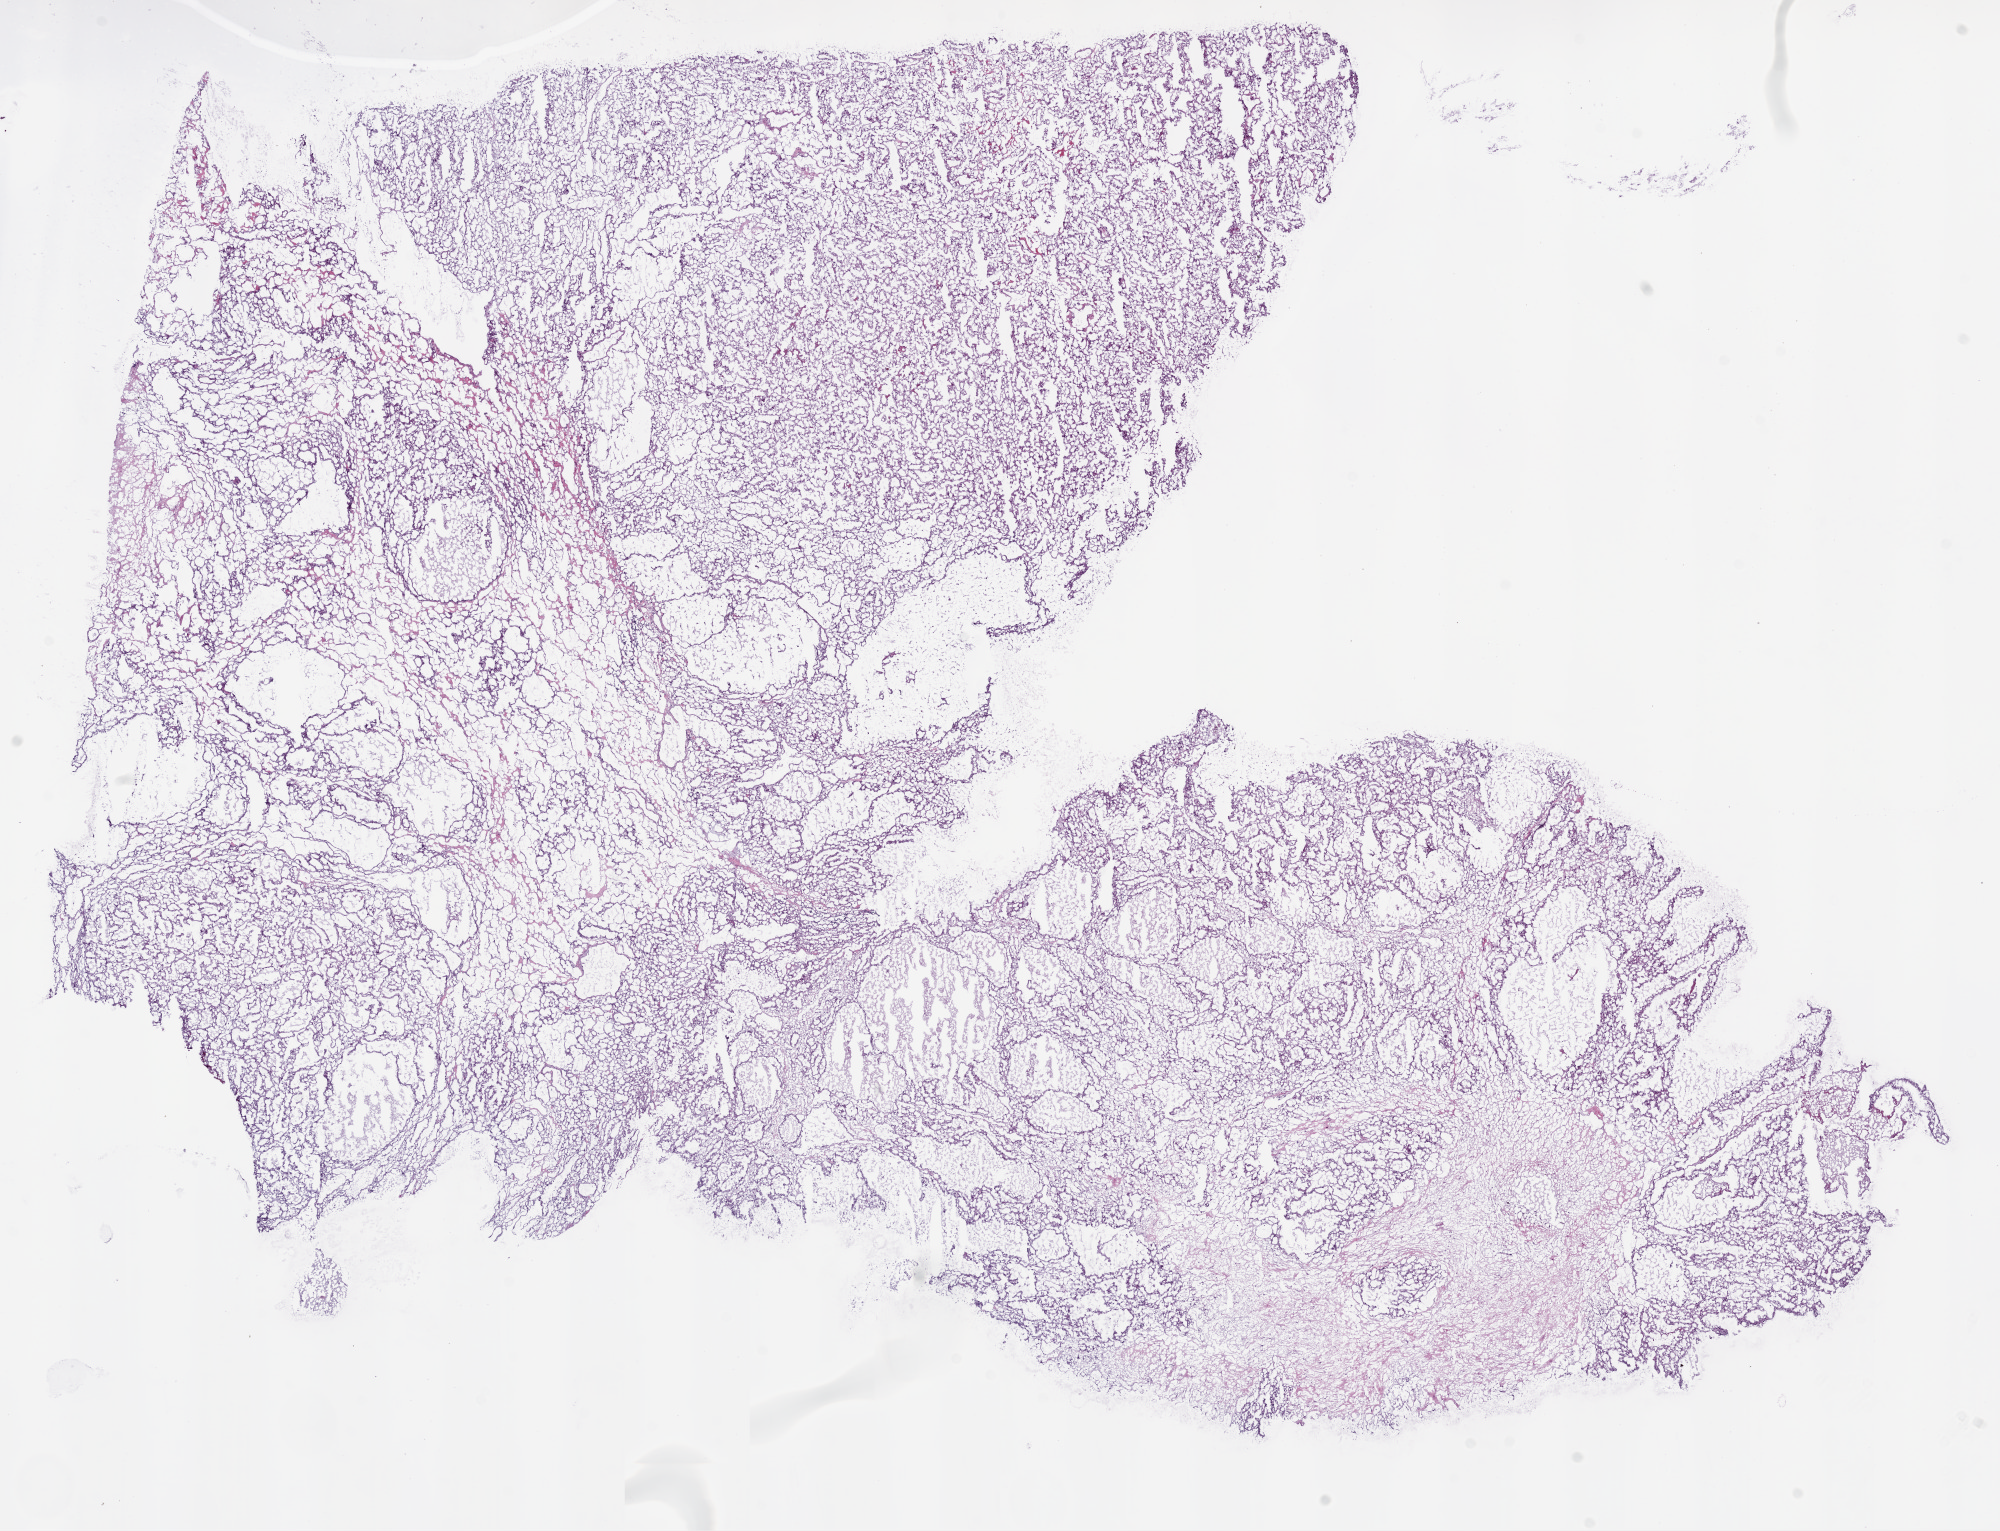
Whole-slide histology image, Hematoxylin and eosin (H&E) stained, shown as a low-resolution overview of the whole scanned area (about 16.0 x 12.3 mm, from a 20x scan). Frozen section from the bottom of the tissue portion. Primary tumour sample from the kidney. Male, age 54 years at initial diagnosis. Histologic grade: G2 (moderately differentiated). Pathologist review of this section (percent, as recorded): tumour cells 85%, tumour nuclei 85%, normal cells 0%, stromal cells 15%, necrosis 0%.
AJCC pathologic stage: I. Histologic diagnosis: Clear cell adenocarcinoma, NOS.